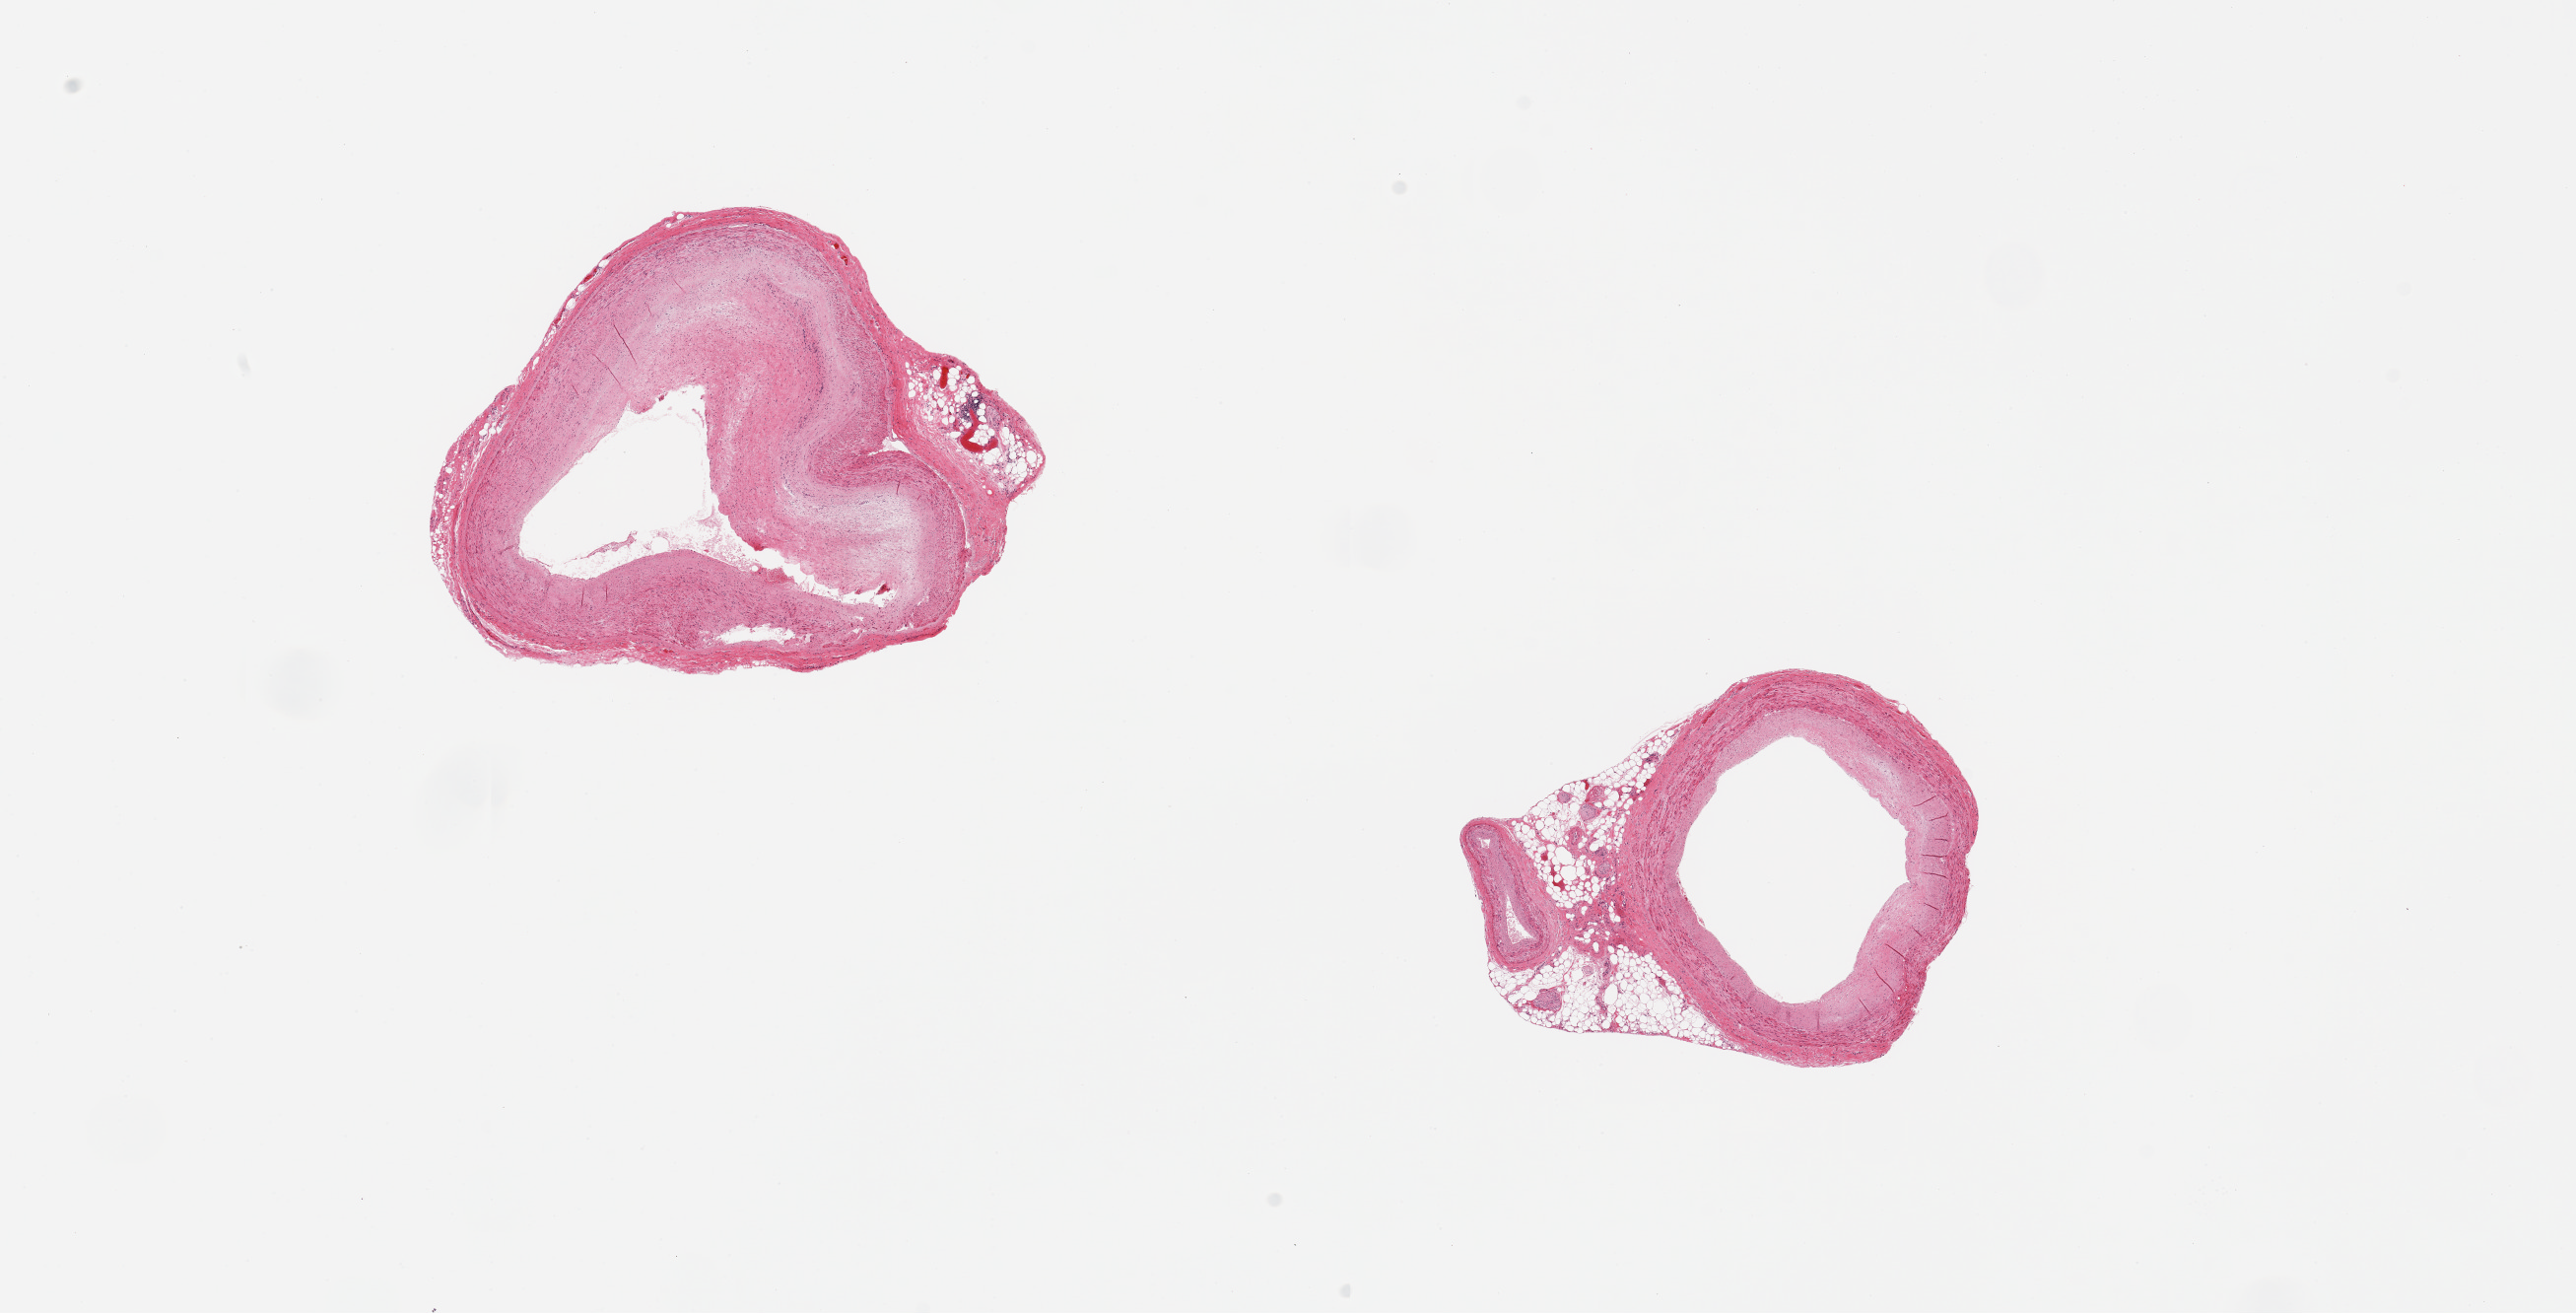
Digitized hematoxylin and eosin (H&E)-stained section, a low-resolution overview of the entire scanned area, about 20.7 x 10.5 mm (slide scanned at 20x), PAXgene-fixed, paraffin-embedded tissue, section of coronary artery (target tissue), donor tissue sample. Male donor.
Reviewer comment on this tissue sample: 2 pieces; moderate plaque formation.